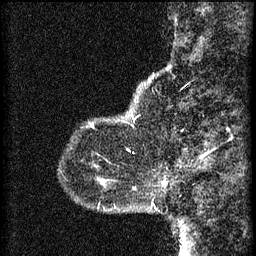
Breast MRI (dynamic contrast-enhanced), one sagittal slice; slice 9 of 60 in the series (ordered by position); 3 images stored at this slice position (order not interpretable as contrast timing); 1.5 T; TE 4.2 ms, TR 8.2 ms; 256 × 256 image matrix, field of view 180 × 180 mm. Female patient, age 37 years.
Structures marked on this image (semi-automatically segmented with operator editing):
- analysis volume of interest (the breast-tissue region the enhancement analysis was run in; not a lesion): bounding box <162,182,165,187> (left, top, right, bottom; pixels)
- tumour enhancement mask (voxels above the 70 % enhancement threshold inside the analysis volume of interest): <162,182,165,185>